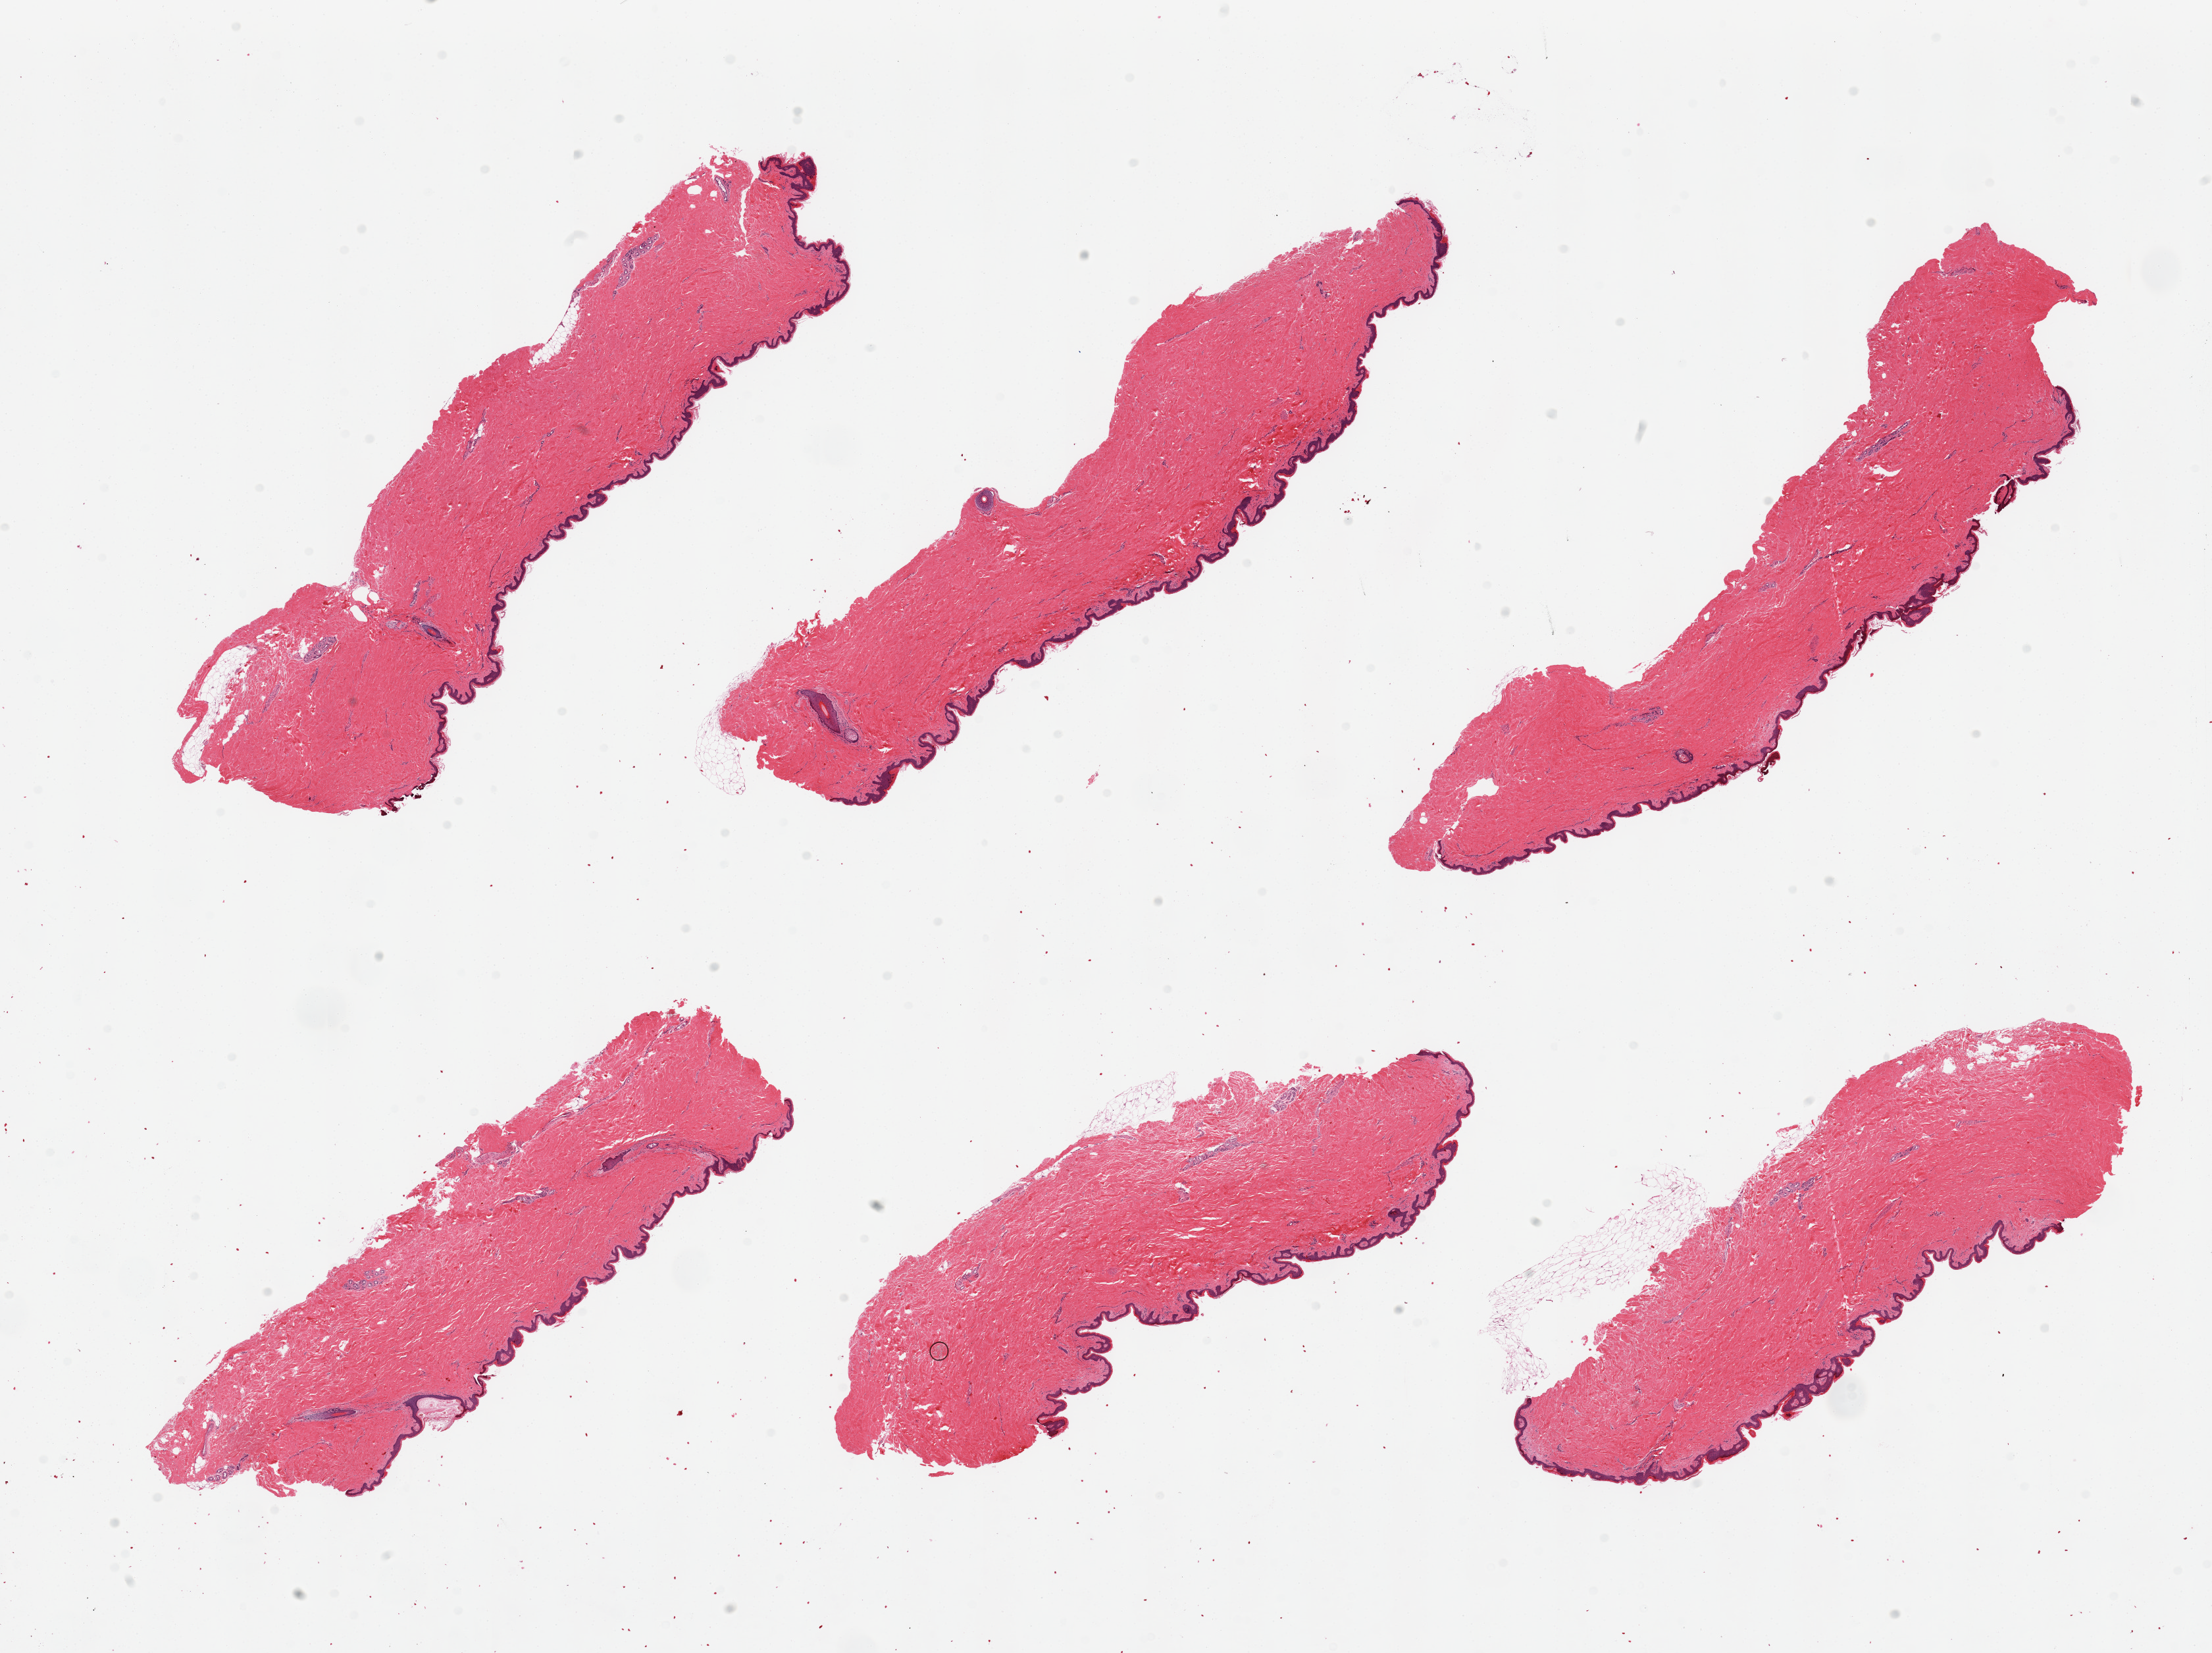
Haematoxylin and eosin whole-slide image, brightfield — whole scanned area (about 26.6 x 19.9 mm) shown as a low-resolution overview. PAXgene-fixed, paraffin-embedded tissue. Target tissue: skin of suprapubic region. Donor tissue sample. Male donor.
* review note (as recorded): 6 pieces, no dermal fat